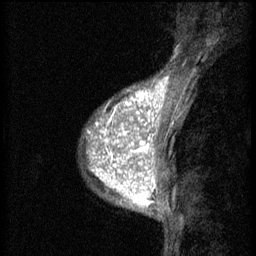
Breast MRI (dynamic contrast-enhanced), one sagittal slice. 3 images stored at this slice position (order not interpretable as contrast timing). 1.5 T. TE 4.2 ms, TR 8.2 ms. 2 mm slice thickness. 256 × 256 image matrix, field of view 180 × 180 mm. Patient: female, 38 years.
Outlined on this slice (semi-automatic segmentation, software-assisted and operator-edited):
- analysis volume of interest (the breast-tissue region the enhancement analysis was run in; not a lesion): box from (x=92, y=112) to (x=152, y=171) px
- tumour enhancement mask (voxels above the 70 % enhancement threshold inside the analysis volume of interest): (x=92, y=112)–(x=152, y=171)